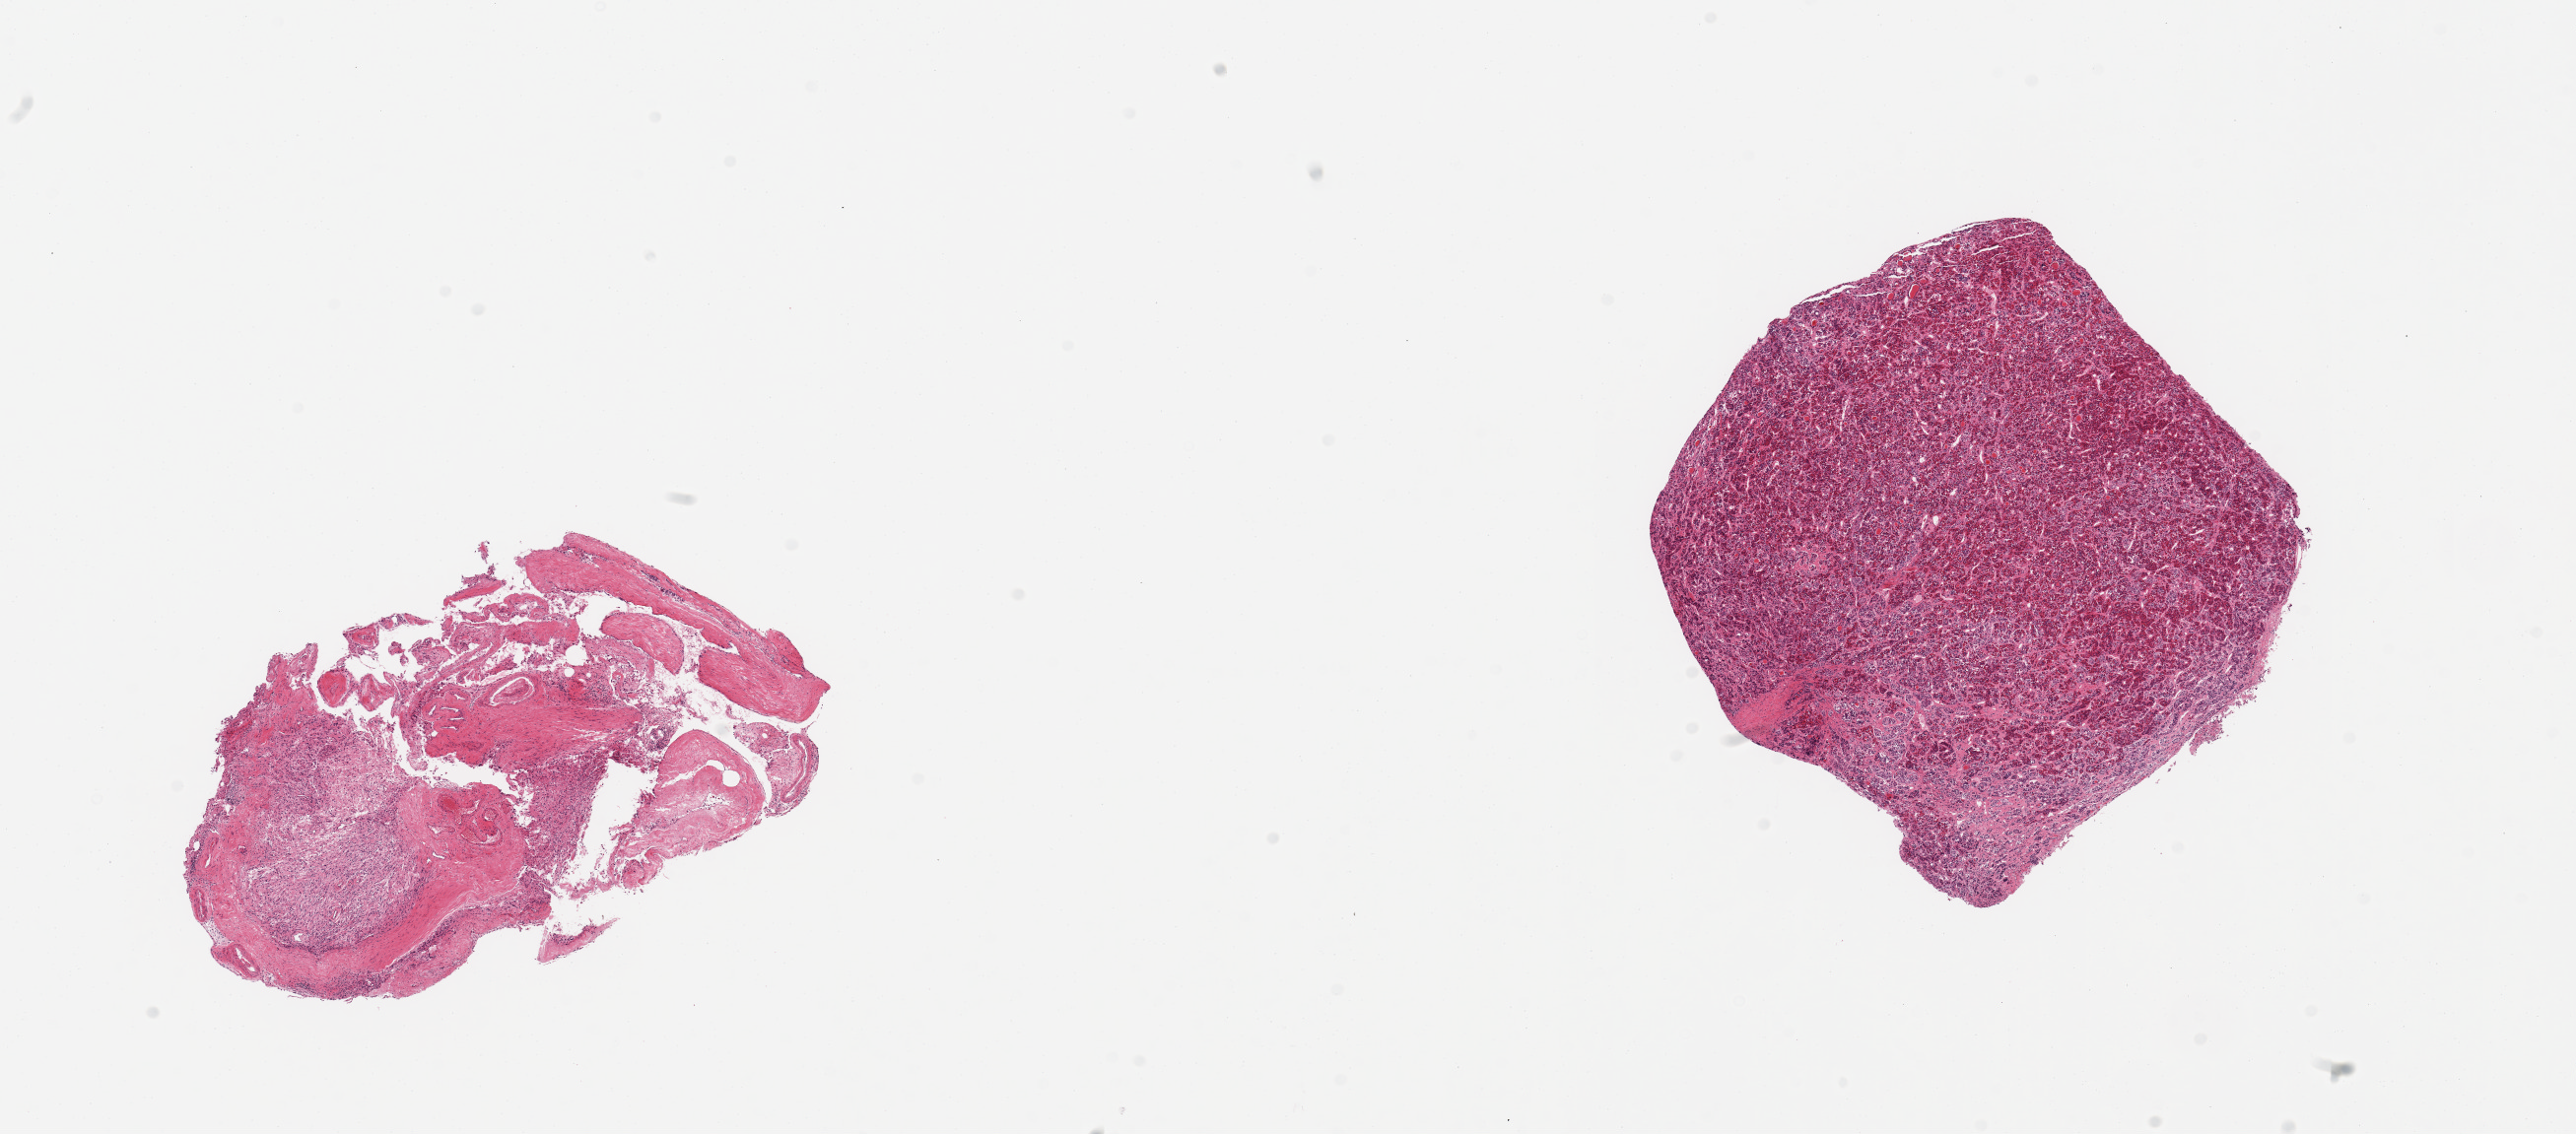
Whole-slide image, haematoxylin and eosin stain — whole scanned area (about 20.7 x 9.1 mm) shown as a low-resolution overview. PAXgene-fixed, paraffin-embedded tissue. Sampled site (target tissue): pituitary. Tissue donor sample. Female donor.
Review note (as recorded): 2 pieces; 1 piece is adenohypophysis, 2nd is fragments of dura and neurohypophysis.